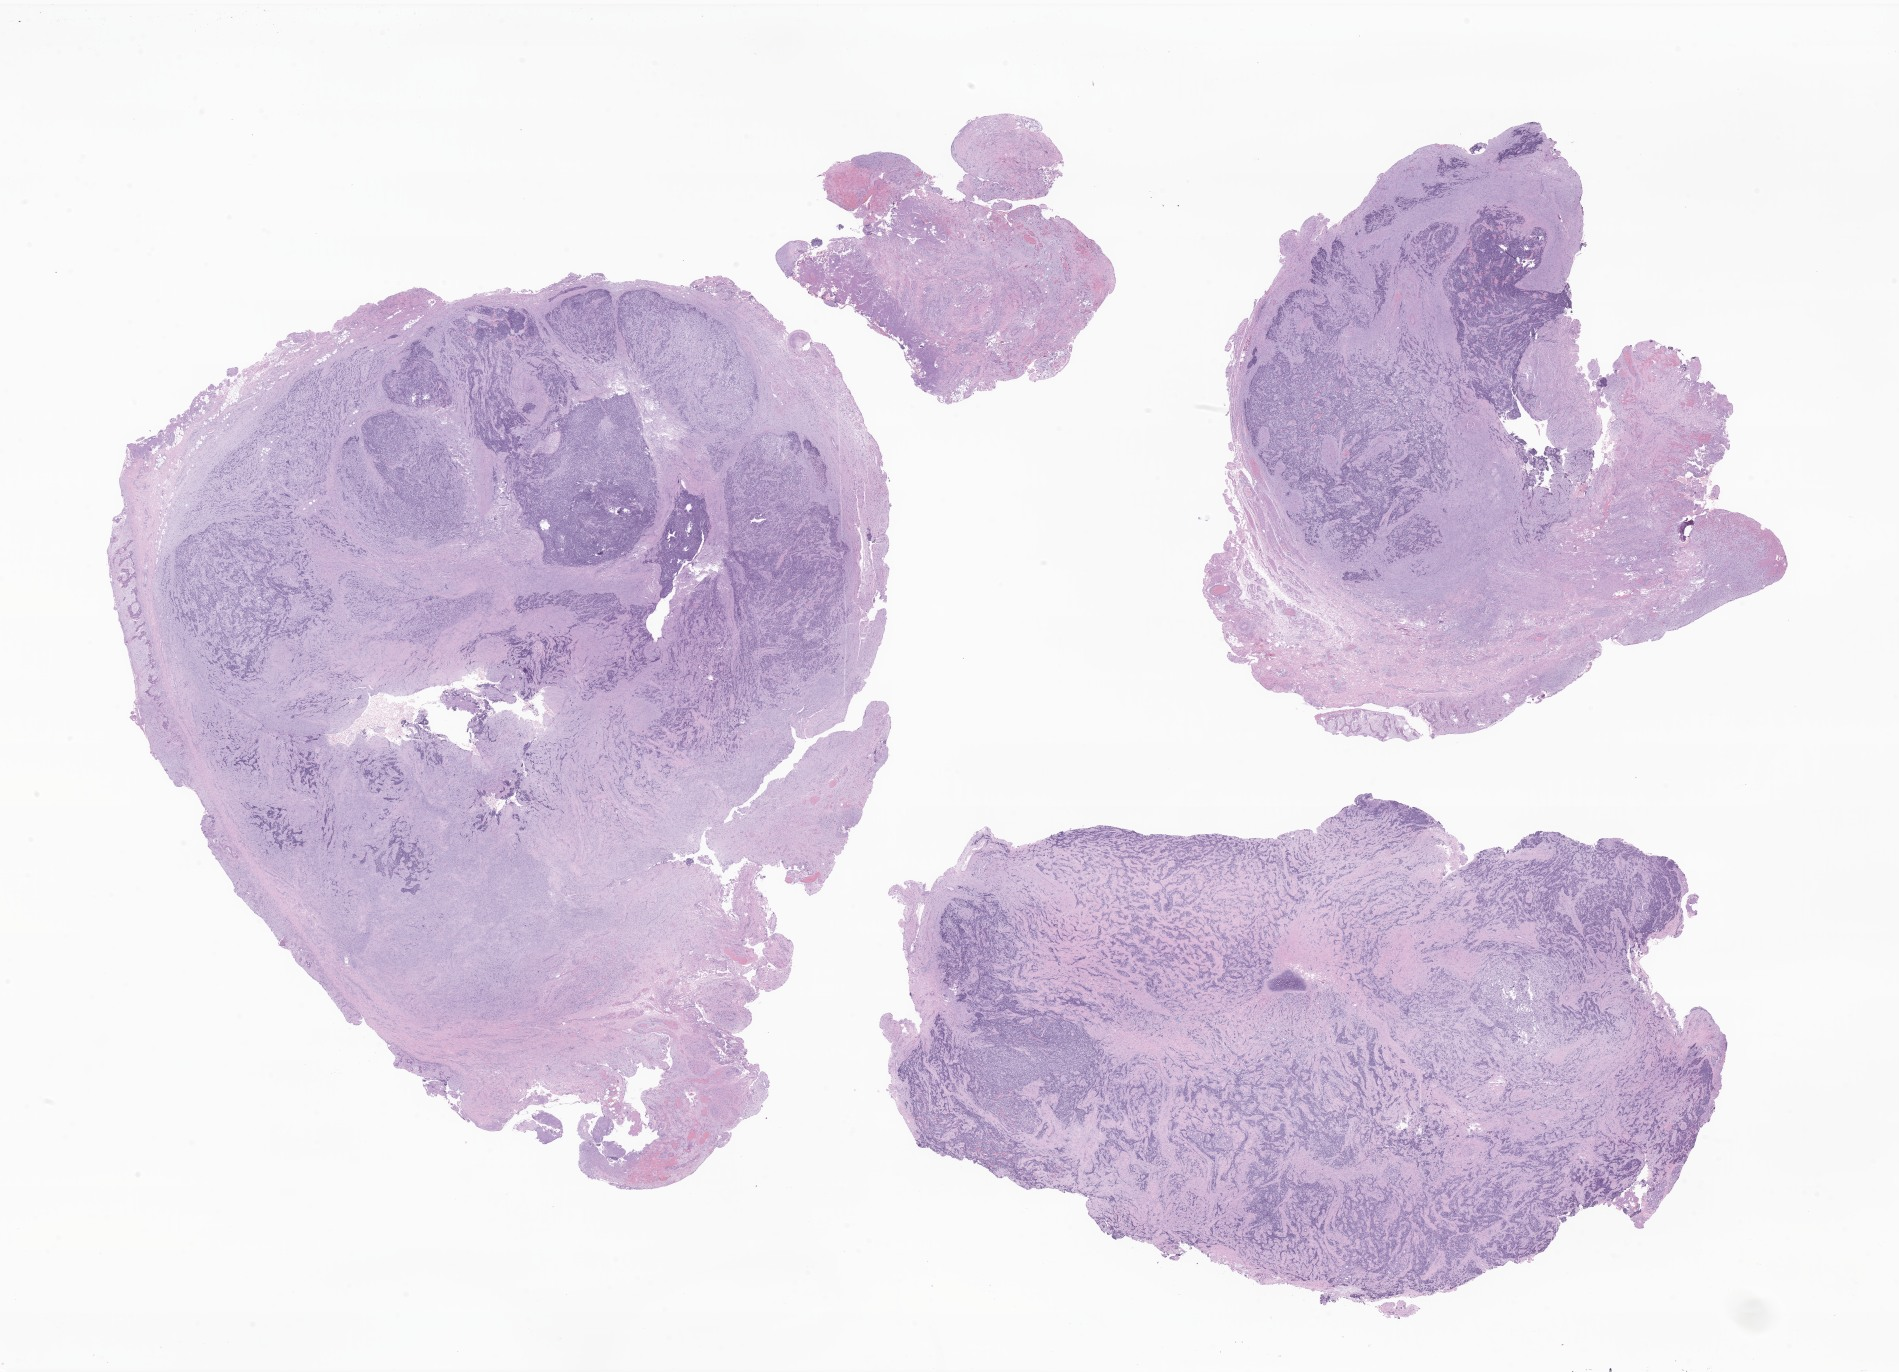
H&E whole-slide image of tumor tissue from the soft tissues of head and neck, whole scanned area (about 32.0 x 23.1 mm) shown as a low-resolution overview; FFPE section. Male patient, age 338 days.
Recorded diagnosis: Rhabdomyosarcoma, NOS. Tissue or organ of origin (case record): connective, subcutaneous and other soft tissues of head, face, and neck.